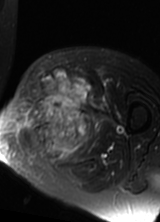
MRI of an extremity soft-tissue mass, one axial slice. Slice 41 of 69 in the series (ordered by position). T2-weighted fat-saturated. MR volume resampled by the dataset authors to the PET/CT grid (not the native acquisition matrix). 160 × 222 image matrix, field of view 156 × 217 mm. Female patient. From the clinical record (not read from this slice): histological type: pleomorphic leiomyosarcoma; grade: high; site of the primary tumour: left thigh.
Annotated regions visible in this slice (expert contour drawn on MRI and transferred to this co-registered scan by the dataset authors):
- gross tumour volume including surrounding oedema: box from (x=20, y=70) to (x=97, y=160) px
- gross tumour volume (mass): (x=29, y=70)–(x=90, y=149)